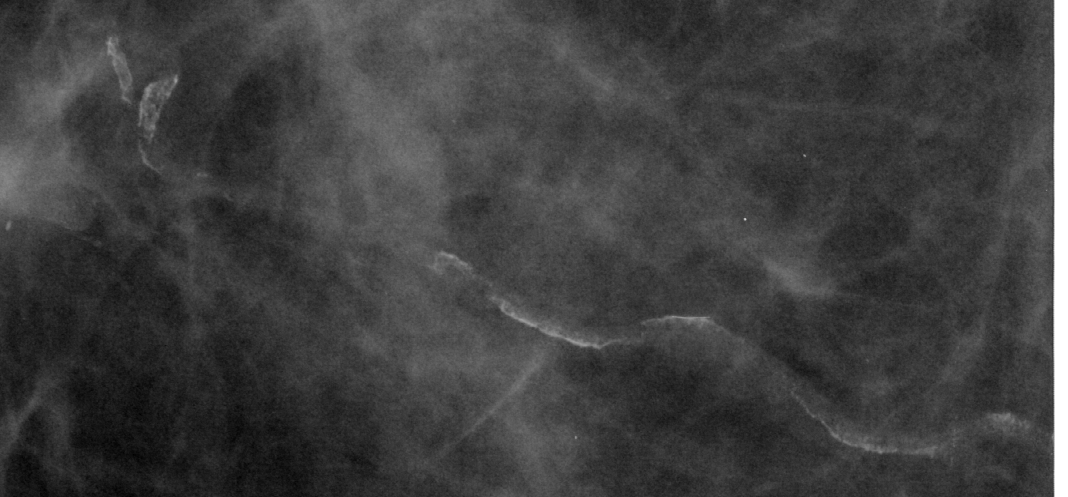
Region of interest cut from a scanned film mammogram (one marked finding); right breast; CC view; BI-RADS breast density category 2 (scale 1–4).
Marked abnormality: calcifications, morphology vascular; BI-RADS assessment category 2; subtlety rating 4 on a 1 (subtle) to 5 (obvious) scale; benign; no additional work-up was recommended (benign without callback).